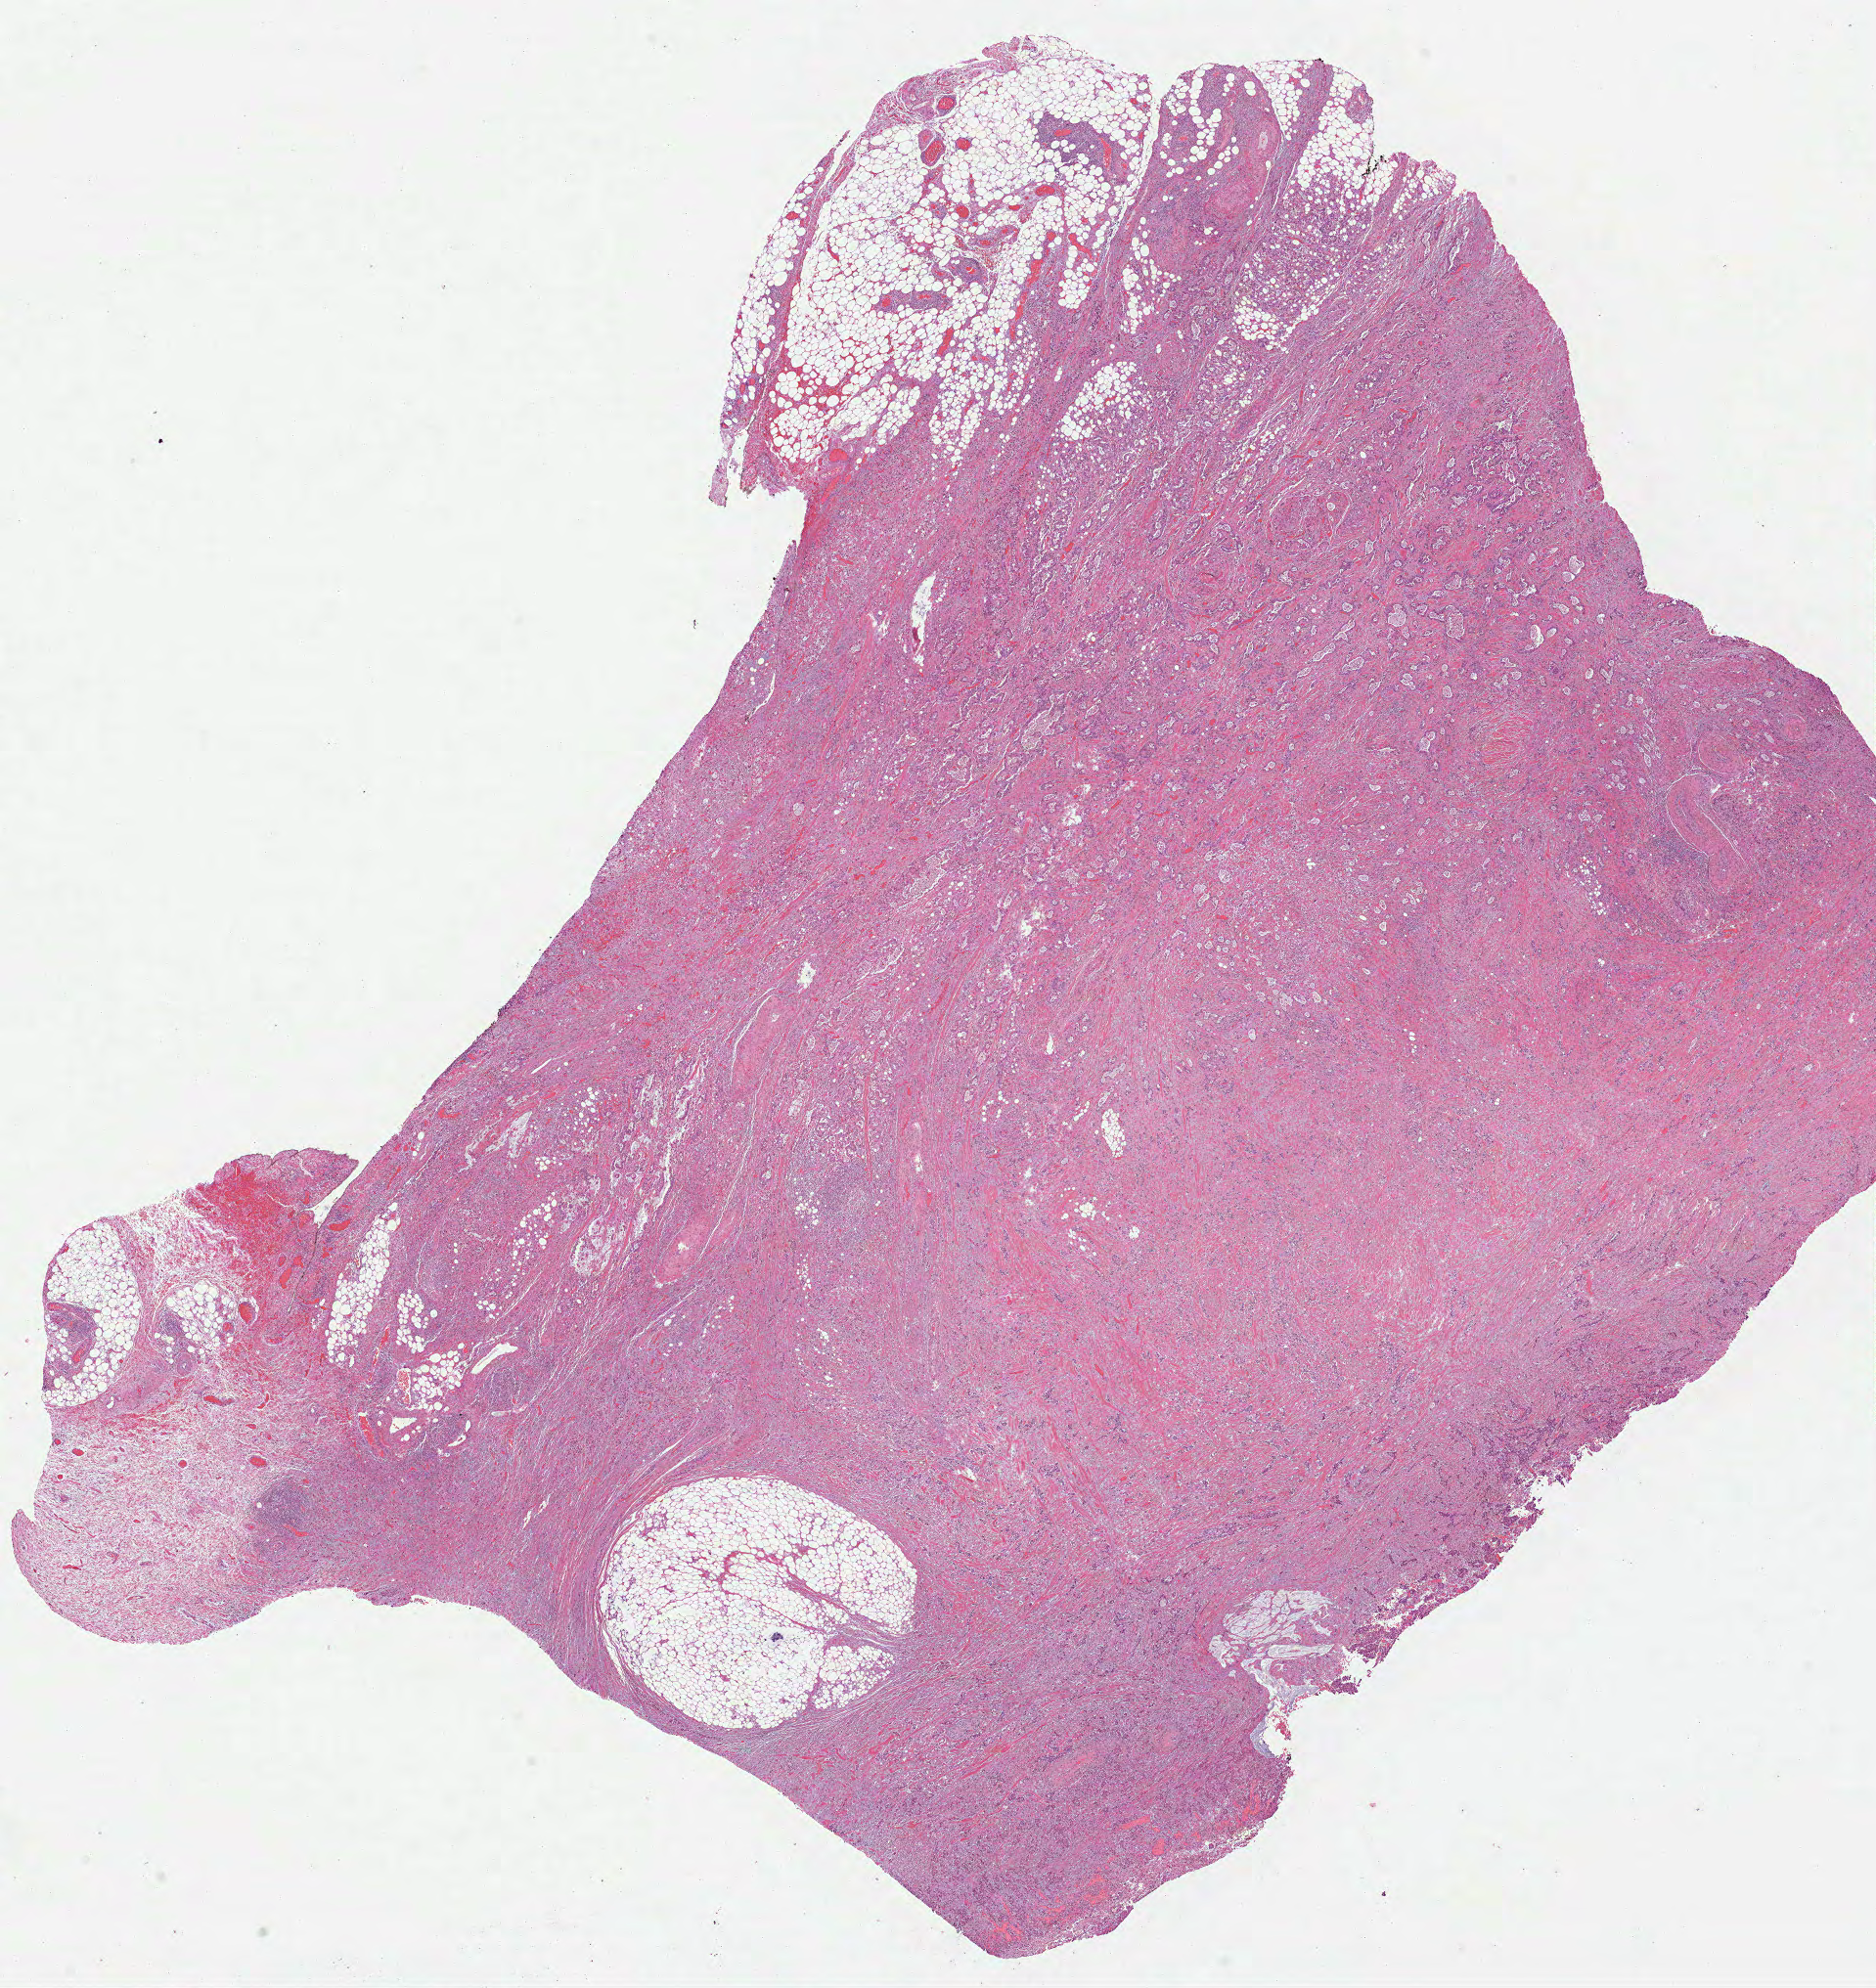
Digitized Hematoxylin and eosin (H&E) stained tissue section (whole slide), whole scanned area (about 15.5 x 16.4 mm, slide scanned at 40x) shown as a low-resolution overview, formalin-fixed paraffin-embedded (FFPE) diagnostic section, primary tumour sample from the stomach. Male patient; age at initial diagnosis 68 years. Histologic grade: G3 (poorly differentiated).
Histologic diagnosis: Signet ring cell carcinoma. AJCC pathologic stage: IIIA.